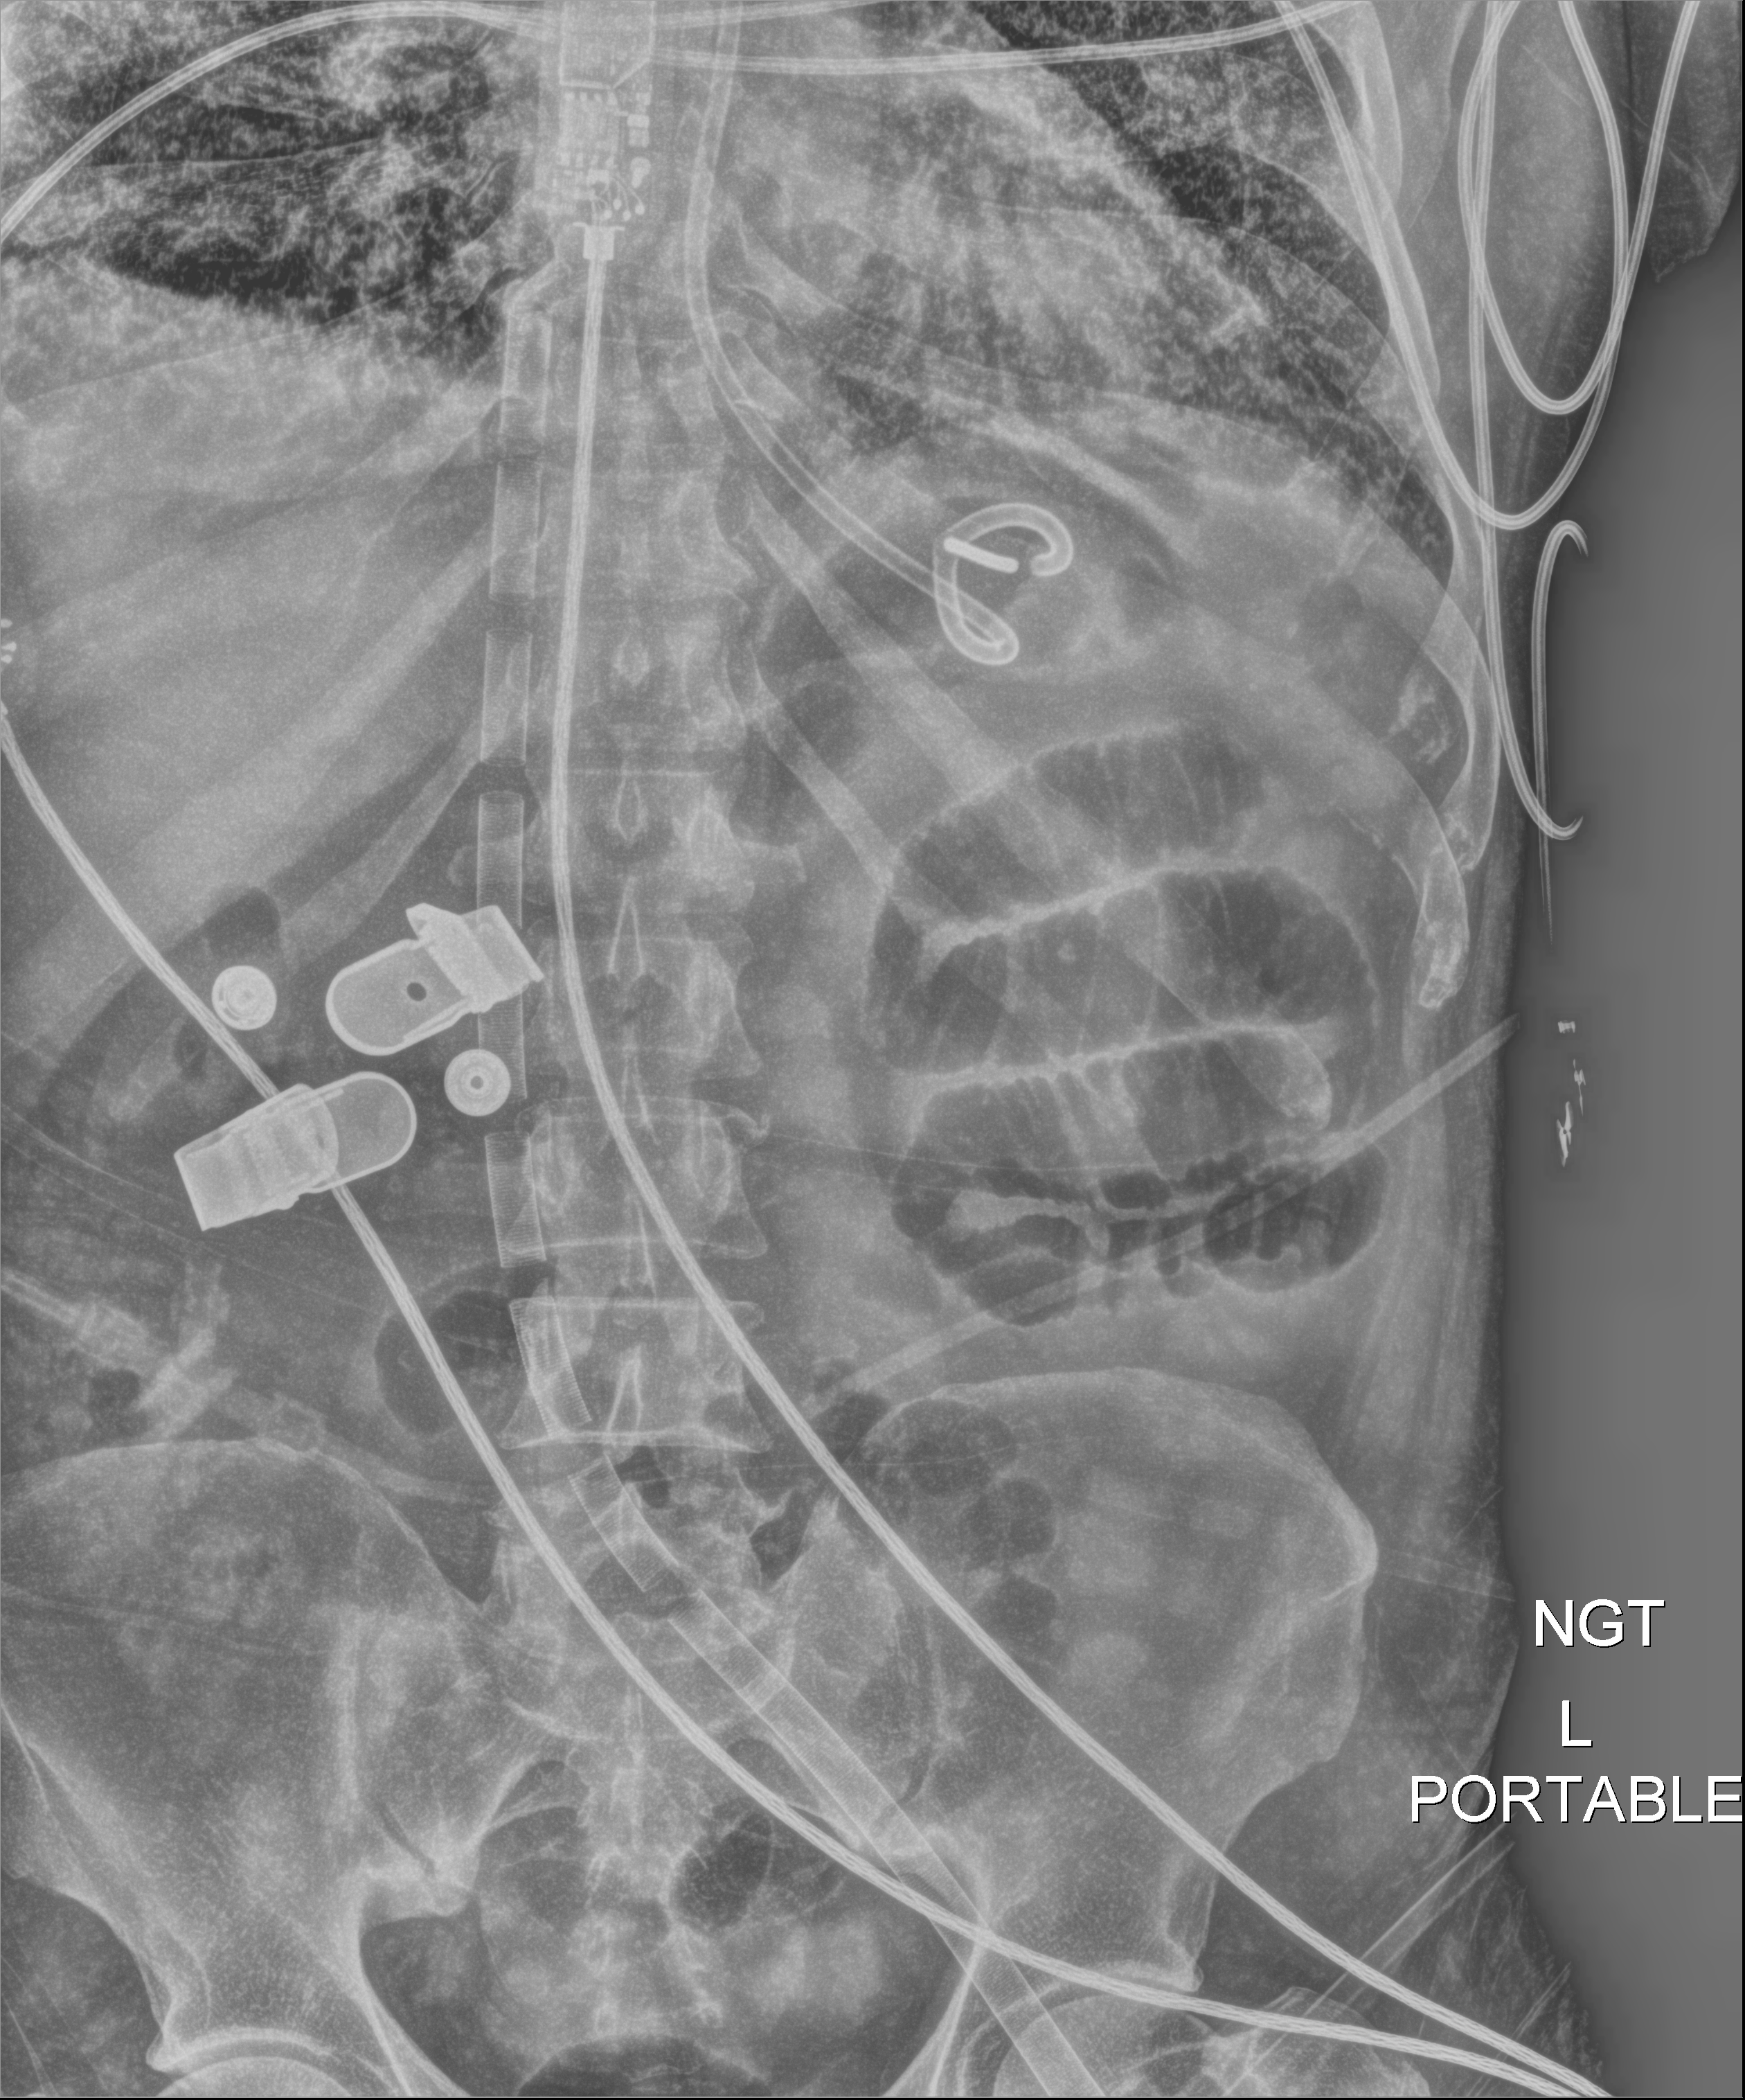
Abdomen radiograph, anteroposterior (AP) projection. Male patient hospitalised with COVID-19, age 18–59 years.
Admission-level facts for this patient (not findings on this image; timing relative to this image not recorded):
- admitted to intensive care during this hospital stay: yes
- mechanically ventilated during this hospital stay: yes